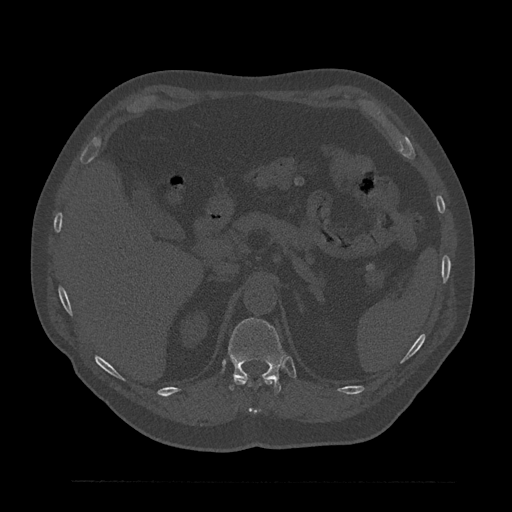
CT including the spine, one axial slice. Reconstruction kernel Br40s/3. Bone window (W 1800 / L 400 HU). 512 × 512 image matrix, field of view 430 × 430 mm. Patient: male, 61 years. From the clinical record (not read from this slice): primary cancer: prostate.
Outlined on this slice (semi-automatic segmentation, software-assisted and operator-edited):
- T11 vertebra: bounding box [x1, y1, x2, y2] px = [233, 377, 275, 414]
- T12 vertebra: [228, 318, 285, 393]